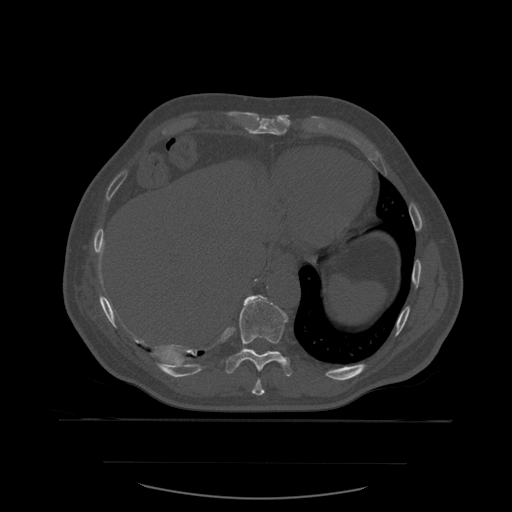
CT including the spine, one axial slice. Bone window (W 1800 / L 400 HU). 1.25 mm slice thickness. 512 × 512 image matrix. Patient age 71 years. From the clinical record (not read from this slice): primary cancer: lung.
Annotated regions visible in this slice (semi-automatically segmented with operator editing):
- T10 vertebra: bounding box (x1, y1, x2, y2) in pixels: (226, 295, 293, 377)
- T9 vertebra: (252, 379, 265, 396)